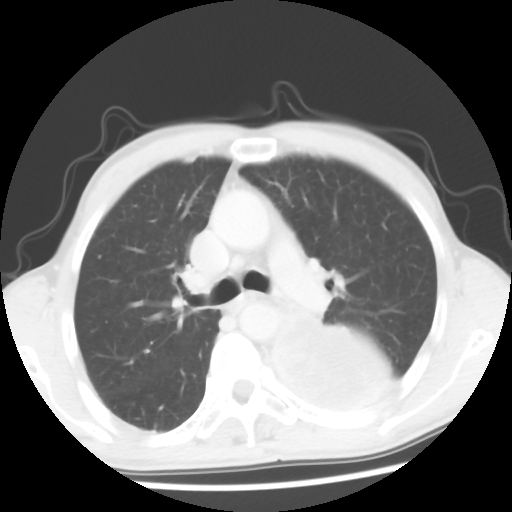
Chest CT, one axial slice. Position 37 of 56 along the scan axis. Reconstruction kernel STANDARD. Lung window (W 1500 / L -600 HU). 5 mm slice thickness. 512 × 512 image matrix. Male patient, age 60 years. Case-level facts recorded for this patient, not image findings: clinical TNM (as recorded): T4 N0 M0.
Annotated regions visible in this slice (rectangle marked by the reading radiologist):
- lung tumour (recorded histology: squamous cell carcinoma): bounding box [x1, y1, x2, y2] px = [259, 318, 395, 418]